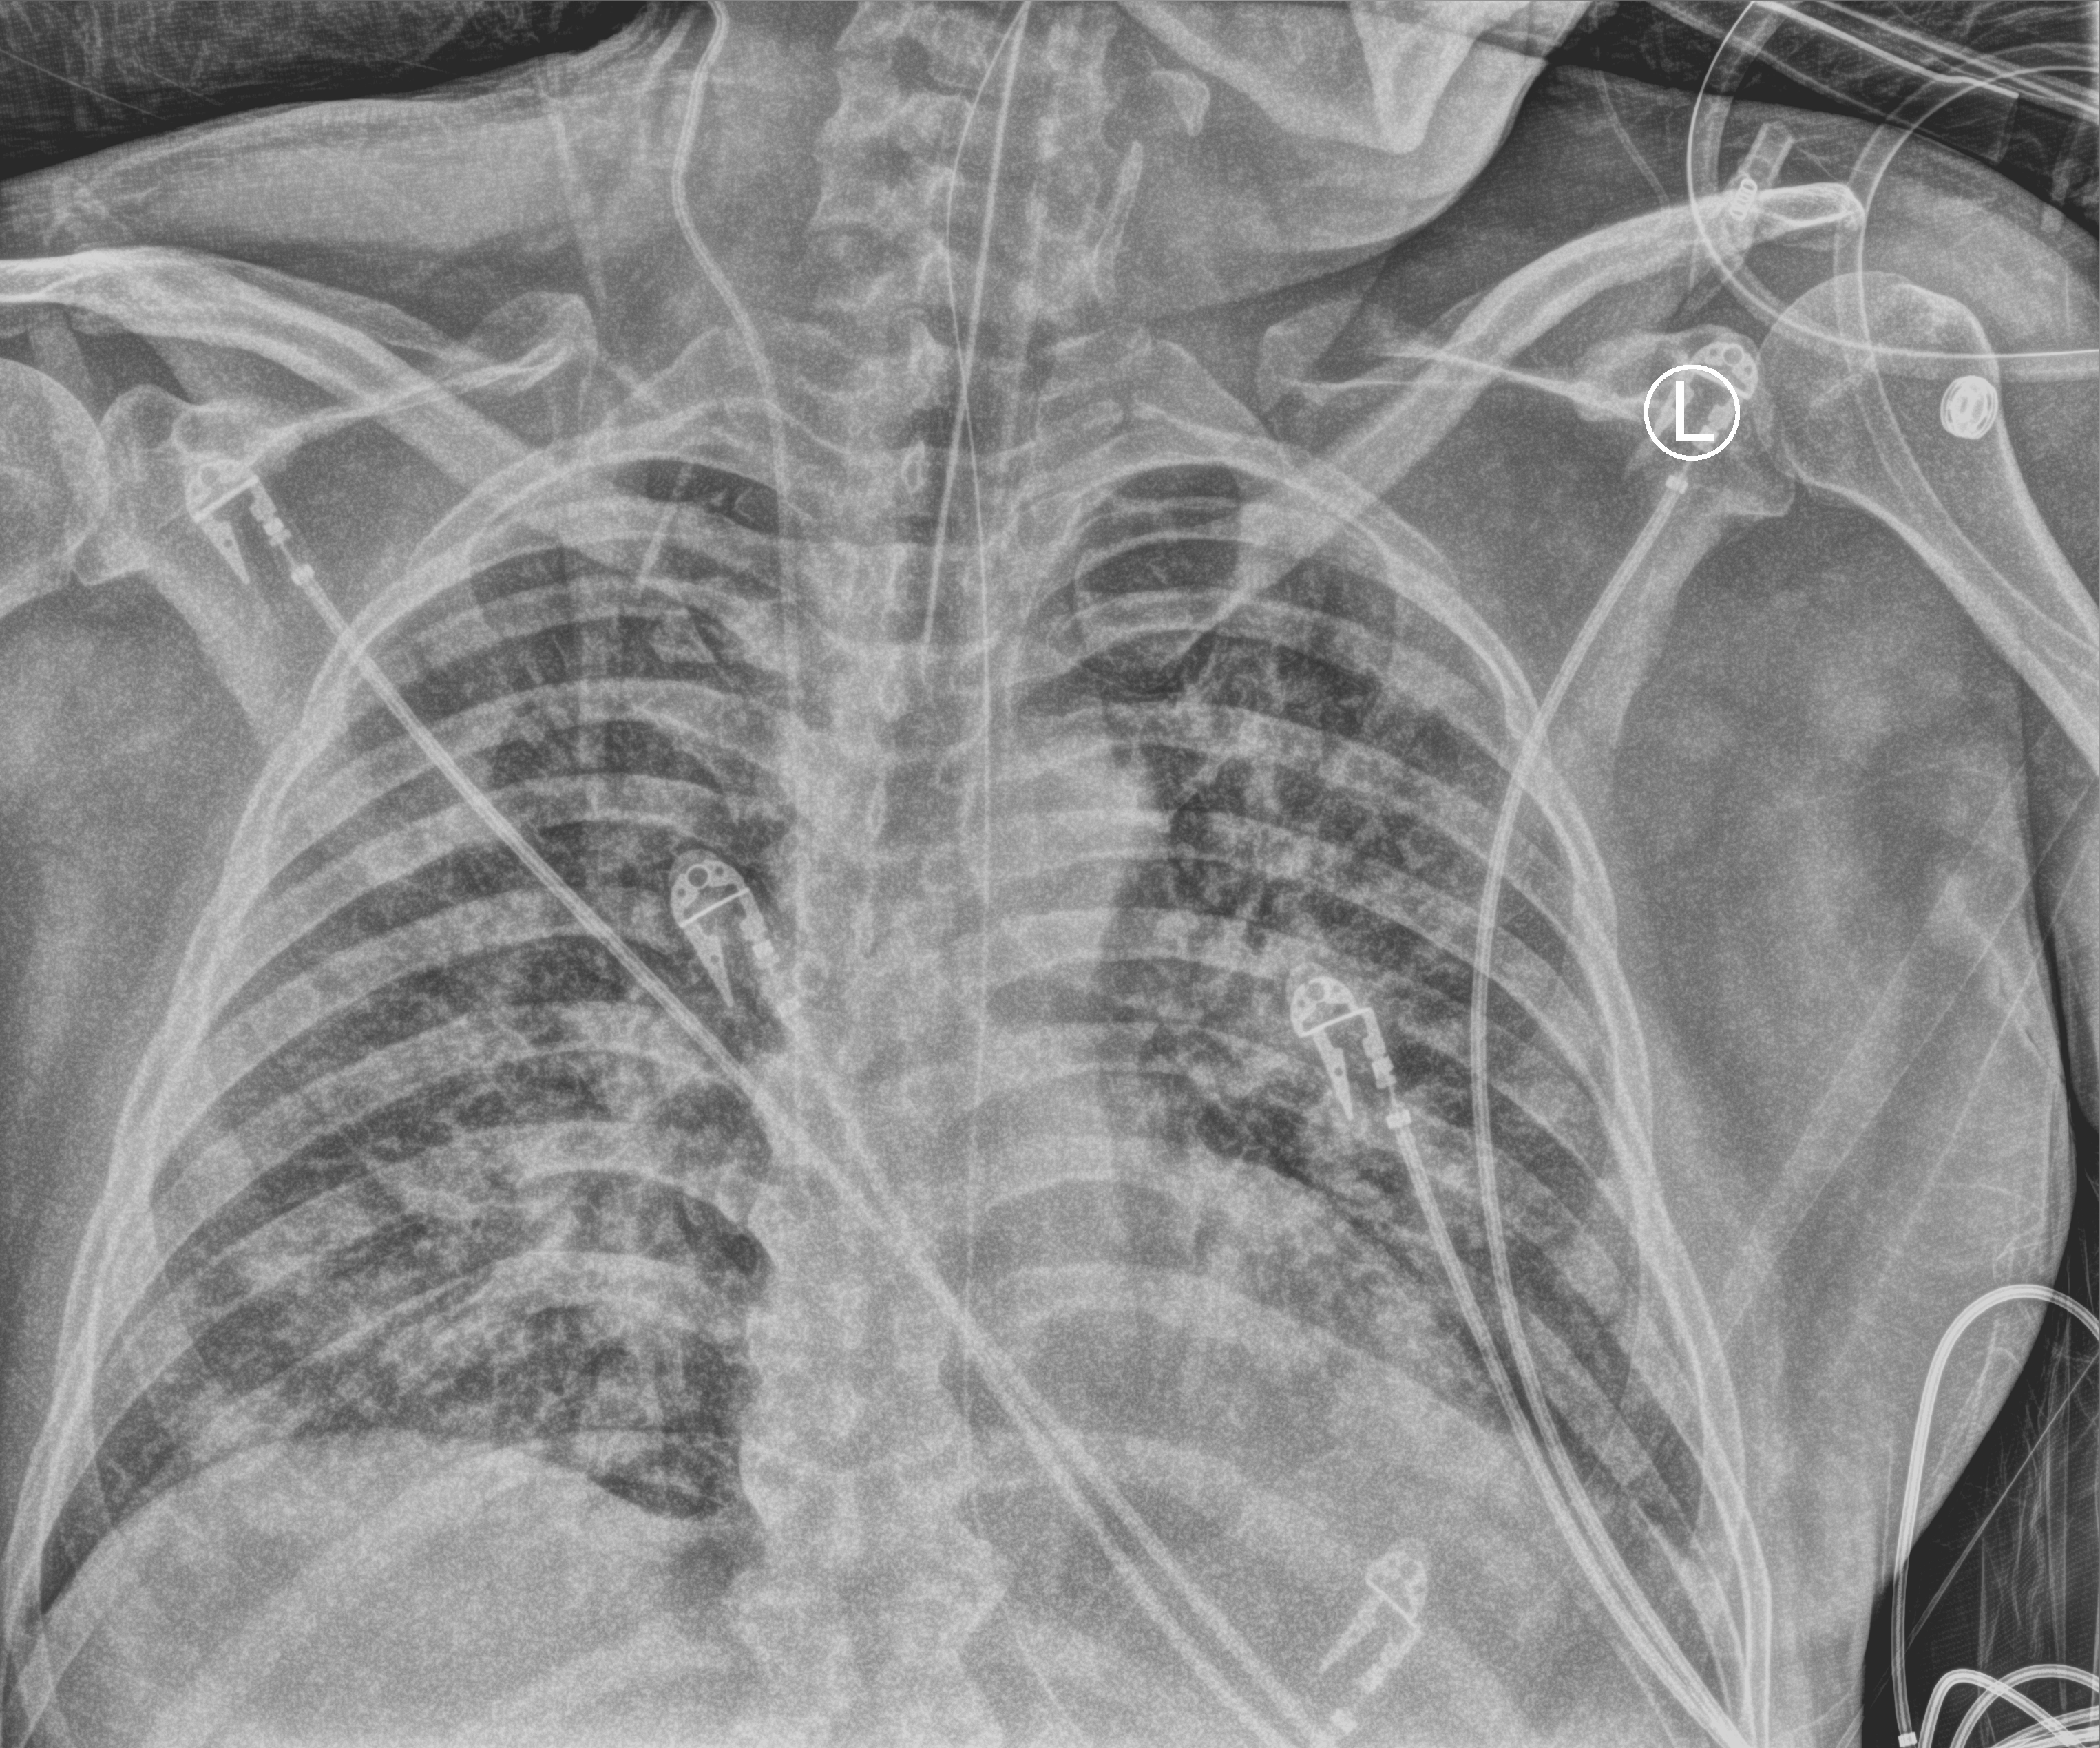
Chest X-ray (portable); anteroposterior (AP) projection. Patient hospitalised with COVID-19; male, aged 18–59 years.
Hospital-stay facts (about this admission, not read from this image; timing relative to this image not recorded): chronic kidney disease (admission record): no.